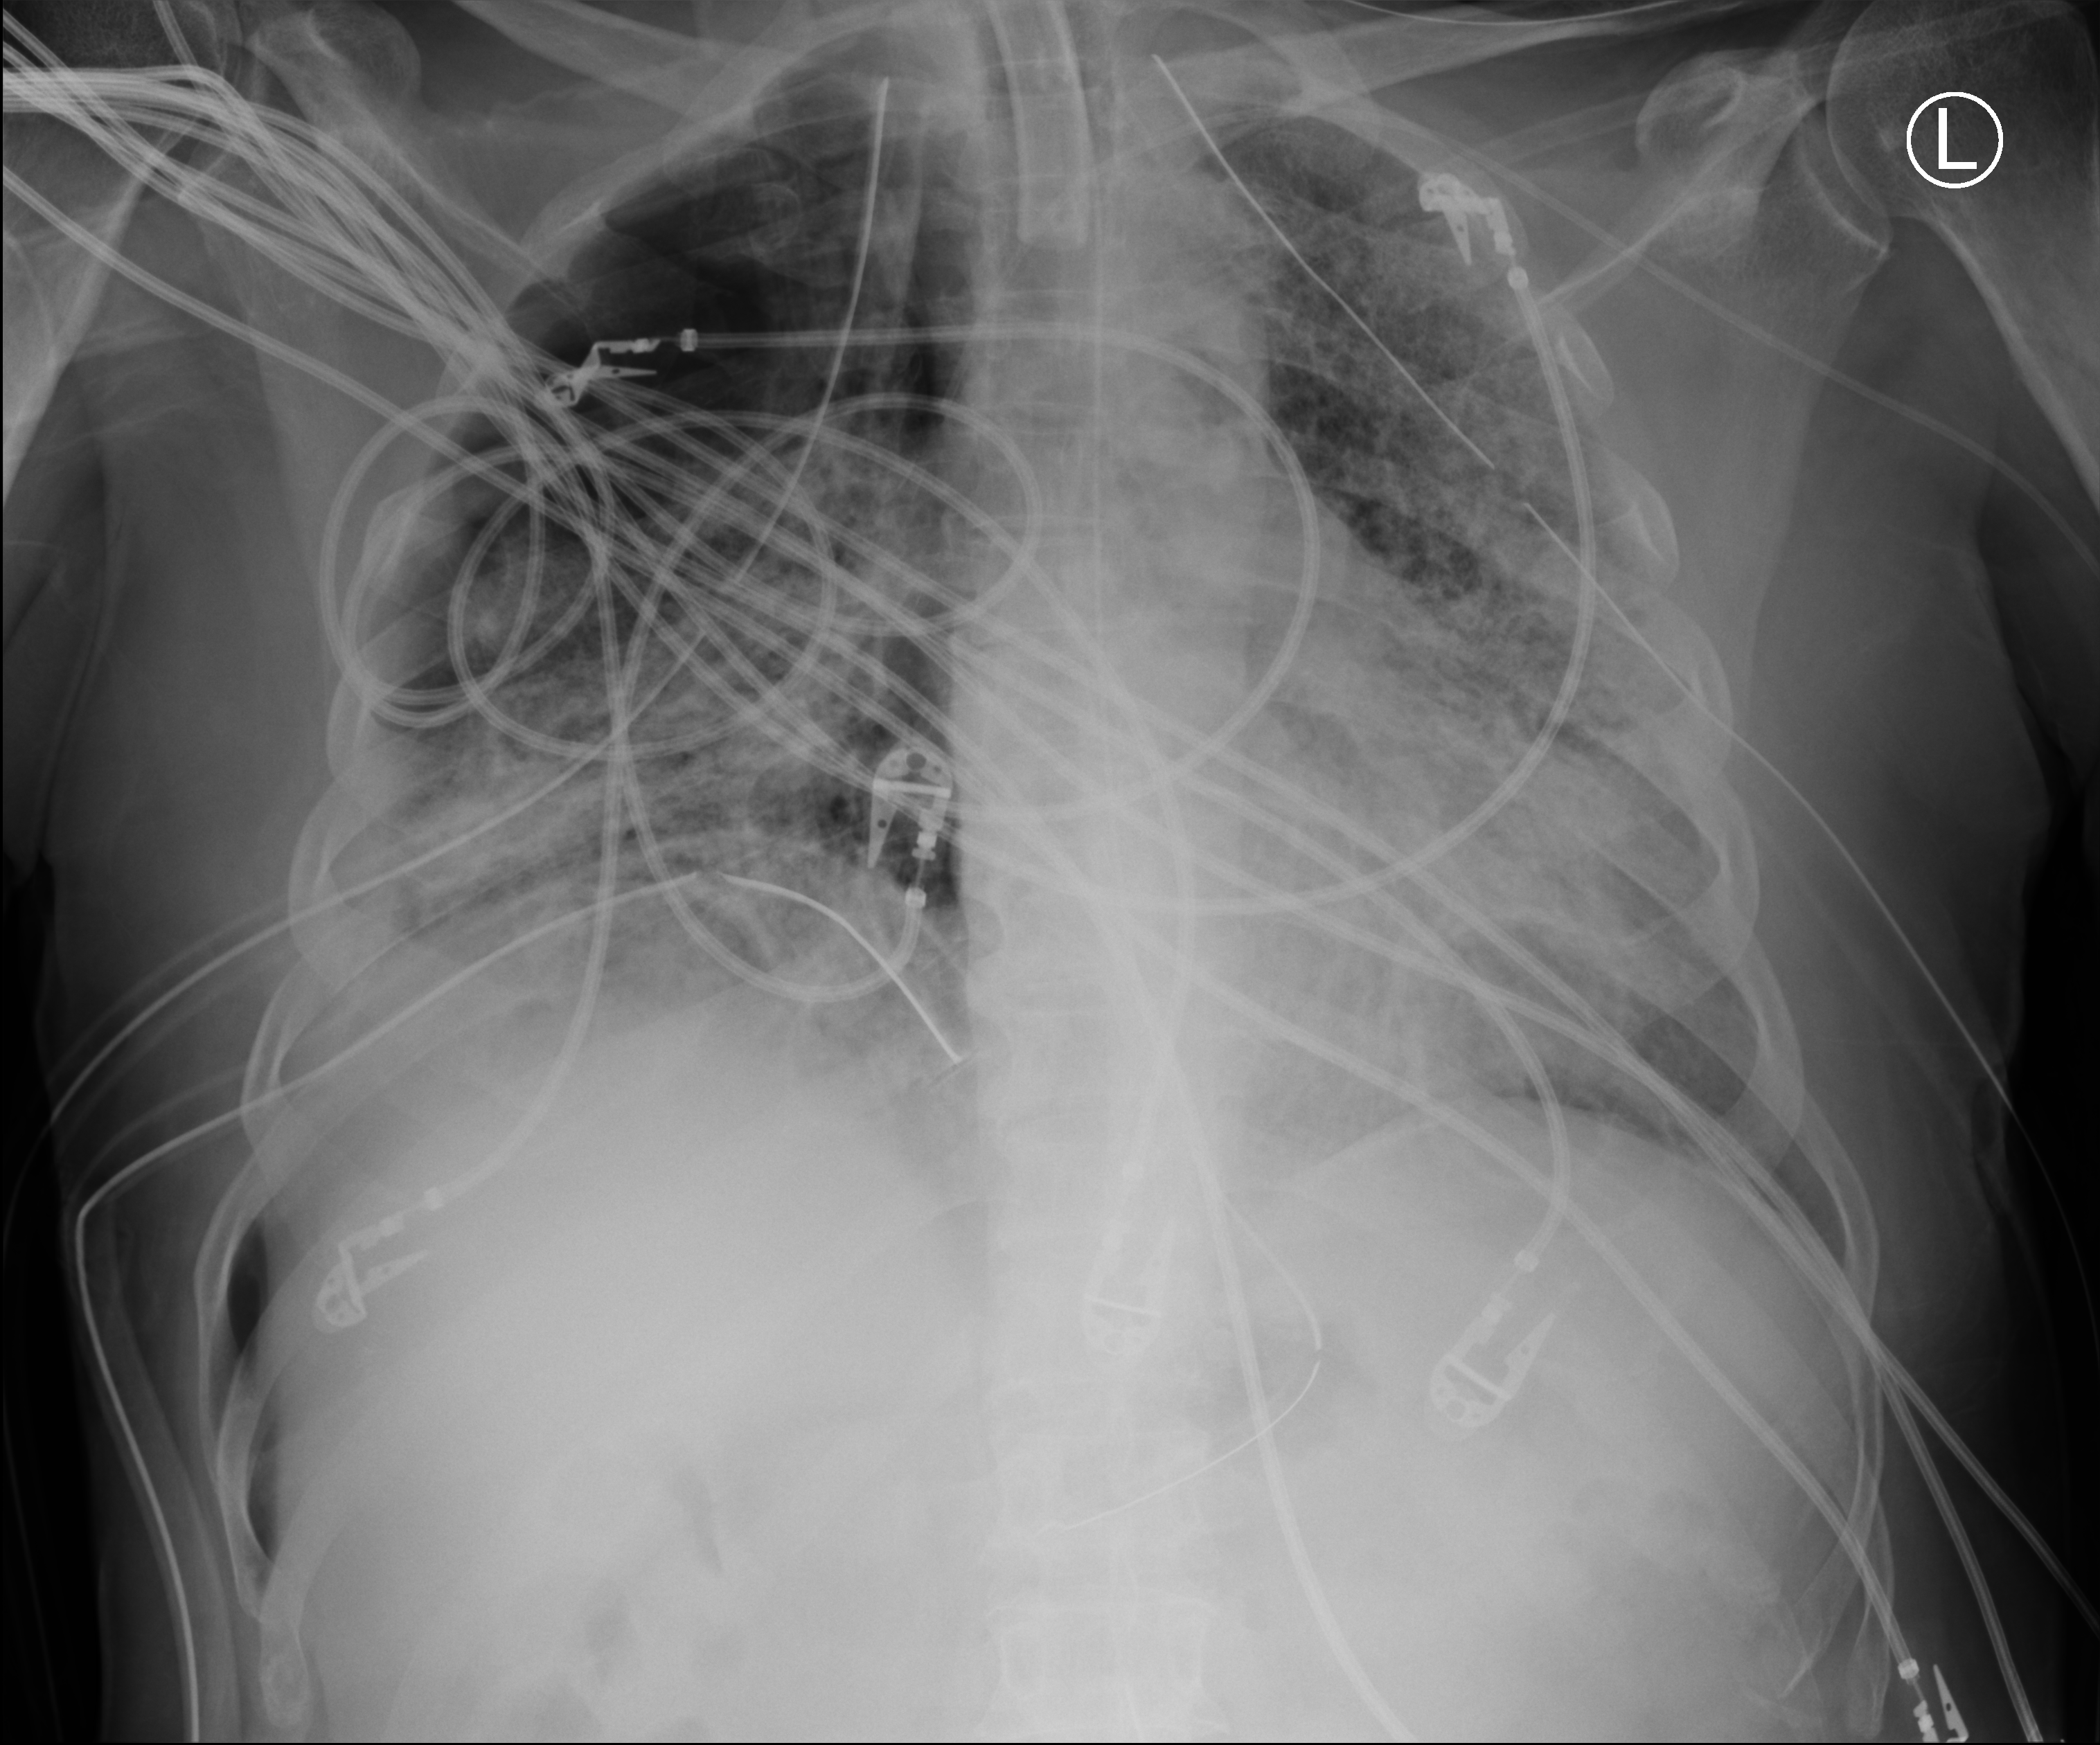
Portable chest radiograph; anteroposterior (AP) projection. Male patient hospitalised with COVID-19, age 18–59 years.
Hospital-stay facts (about this admission, not read from this image; timing relative to this image not recorded):
- admitted to intensive care during this hospital stay: yes